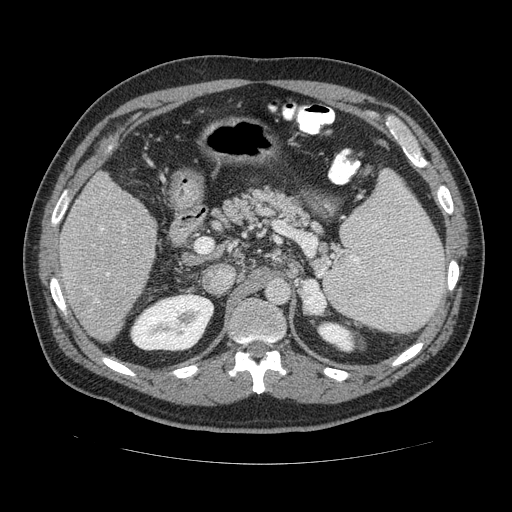
Contrast-enhanced abdominal CT (liver protocol), one axial slice. Slice 71 of 113 in the series (ordered by position). 120 kVp. Soft-tissue window (W 400 / L 40 HU). 2.5 mm slice thickness. 512 × 512 image matrix. Case-level facts recorded for this patient, not image findings: diagnosis: hepatocellular carcinoma (patient treated with transarterial chemoembolisation; whether this scan precedes or follows treatment is not stated here); TNM stage (as recorded): Stage-II; Child-Pugh class: B; tumour nodularity: multinodular.
Annotated regions visible in this slice (semi-automatic segmentation, software-assisted and operator-edited):
- liver parenchyma outside the tumour (the mass and vessels are separate outlines, so this box may not span the whole liver): bounding box (x1, y1, x2, y2) in pixels: (52, 168, 158, 344)
- liver vessels: (91, 219, 156, 299)